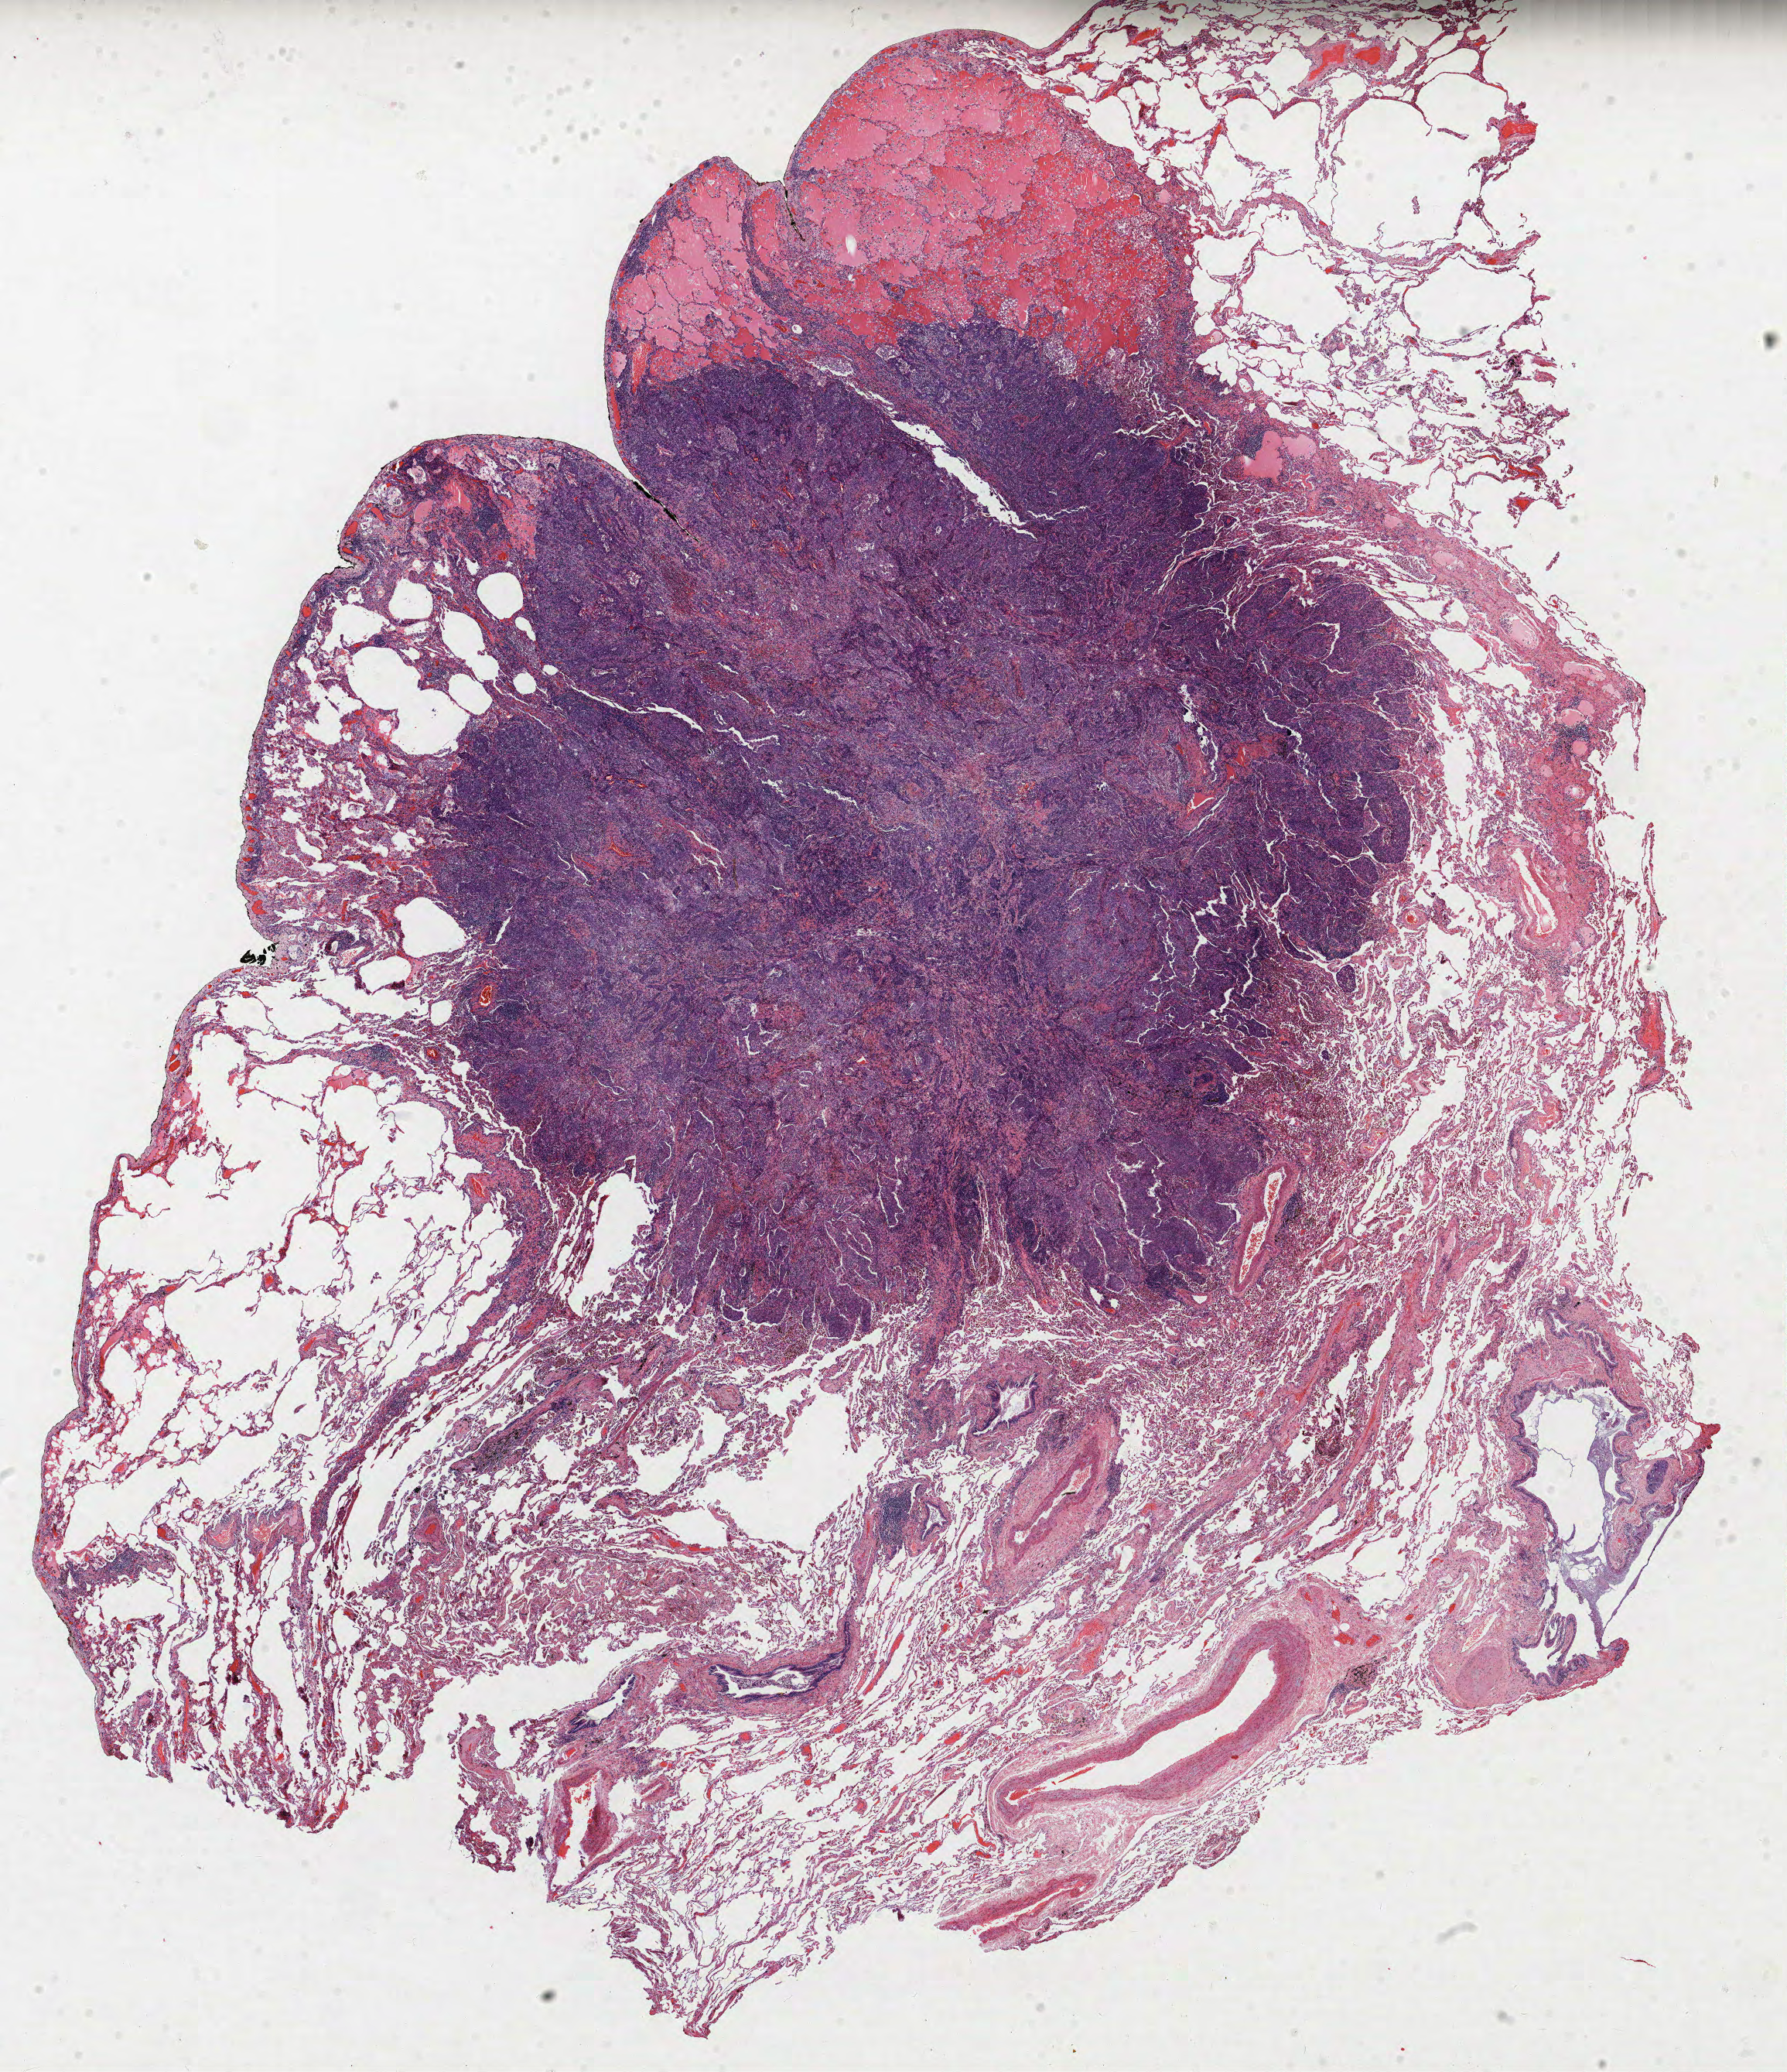
H&E whole-slide image — a low-resolution overview of the entire scanned area, about 18.5 x 21.4 mm (acquisition: 40x scan); FFPE section; lung tissue. Male patient, aged 59 at enrolment. Grade: poorly differentiated (G3).
- tumour size (pathology): 11 mm
- ICD-O-3 topography: upper lobe of lung (C34.1)
- participant's lung-cancer diagnosis: Adenocarcinoma, NOS
- primary tumour location (clinical record): left upper lobe
- stage (AJCC 6th edition): IA